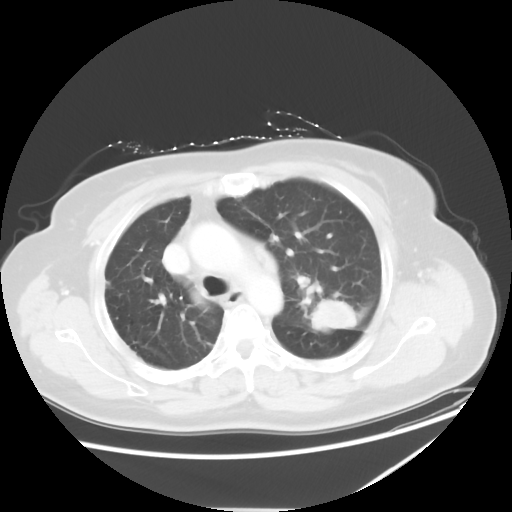
Chest CT, one axial slice; slice 38 of 54 in the series (ordered by position); 120 kVp; lung window (W 1500 / L -600 HU); 5 mm slice thickness; 512 × 512 image matrix. Patient: female, 61 years. From the clinical record (not read from this slice): clinical TNM (as recorded): T1c N3 M1.
Structures marked on this image (rectangle marked by the reading radiologist):
- lung tumour (recorded histology: adenocarcinoma): bounding box <306,296,361,336> (left, top, right, bottom; pixels)